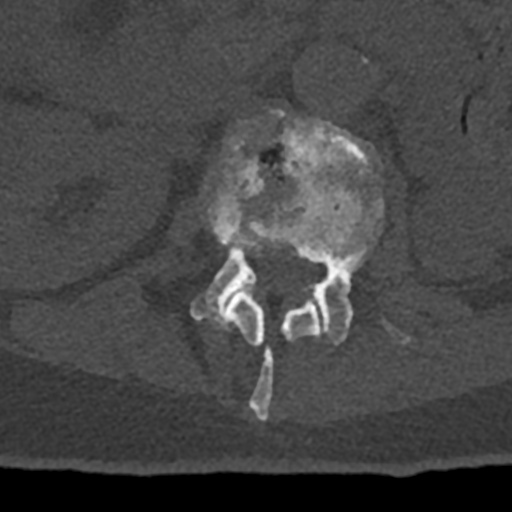
CT including the spine, one axial slice. Position 403 of 797 along the scan axis. 120 kVp. Bone window (W 1800 / L 400 HU). 512 × 512 image matrix, field of view 160 × 160 mm. Patient: male, 74 years. From the clinical record (not read from this slice): primary cancer: renal; vertebrae with lytic lesions (as recorded): T10, L1, L2, L3, L4, L5.
Outlined on this slice (semi-automatically segmented with operator editing):
- L1 vertebra: bounding box (x1, y1, x2, y2) in pixels: (204, 131, 320, 420)
- L2 vertebra: (190, 110, 411, 344)